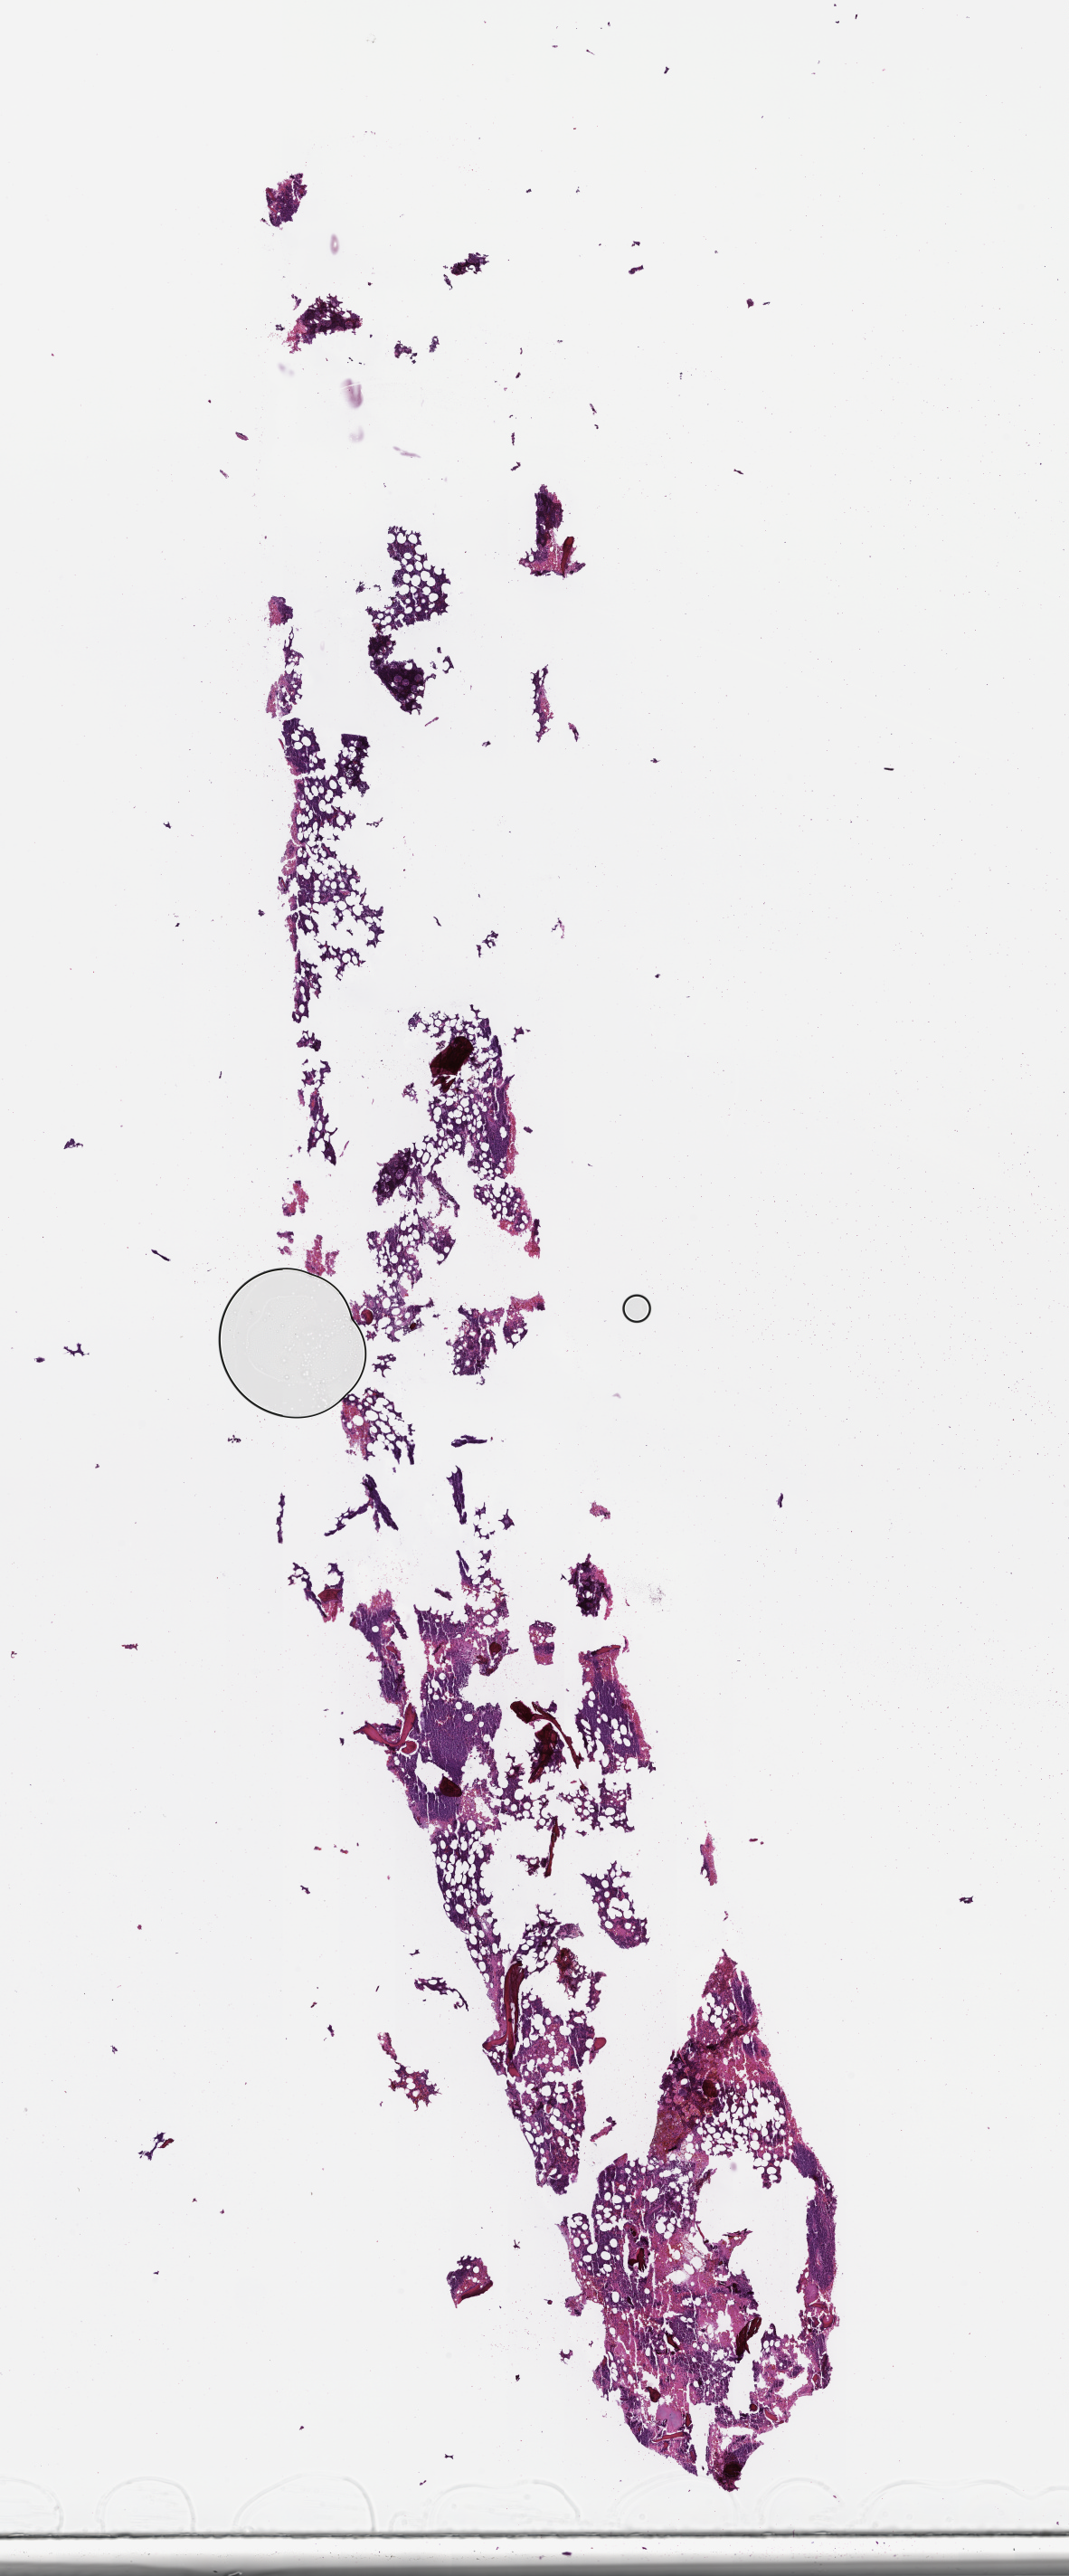
H&E whole-slide image, whole scanned area (about 9.5 x 23.0 mm) shown as a low-resolution overview, FFPE section, tissue site: bone marrow. Patient sex: male.
From a patient with: Plasma Cell Myeloma.